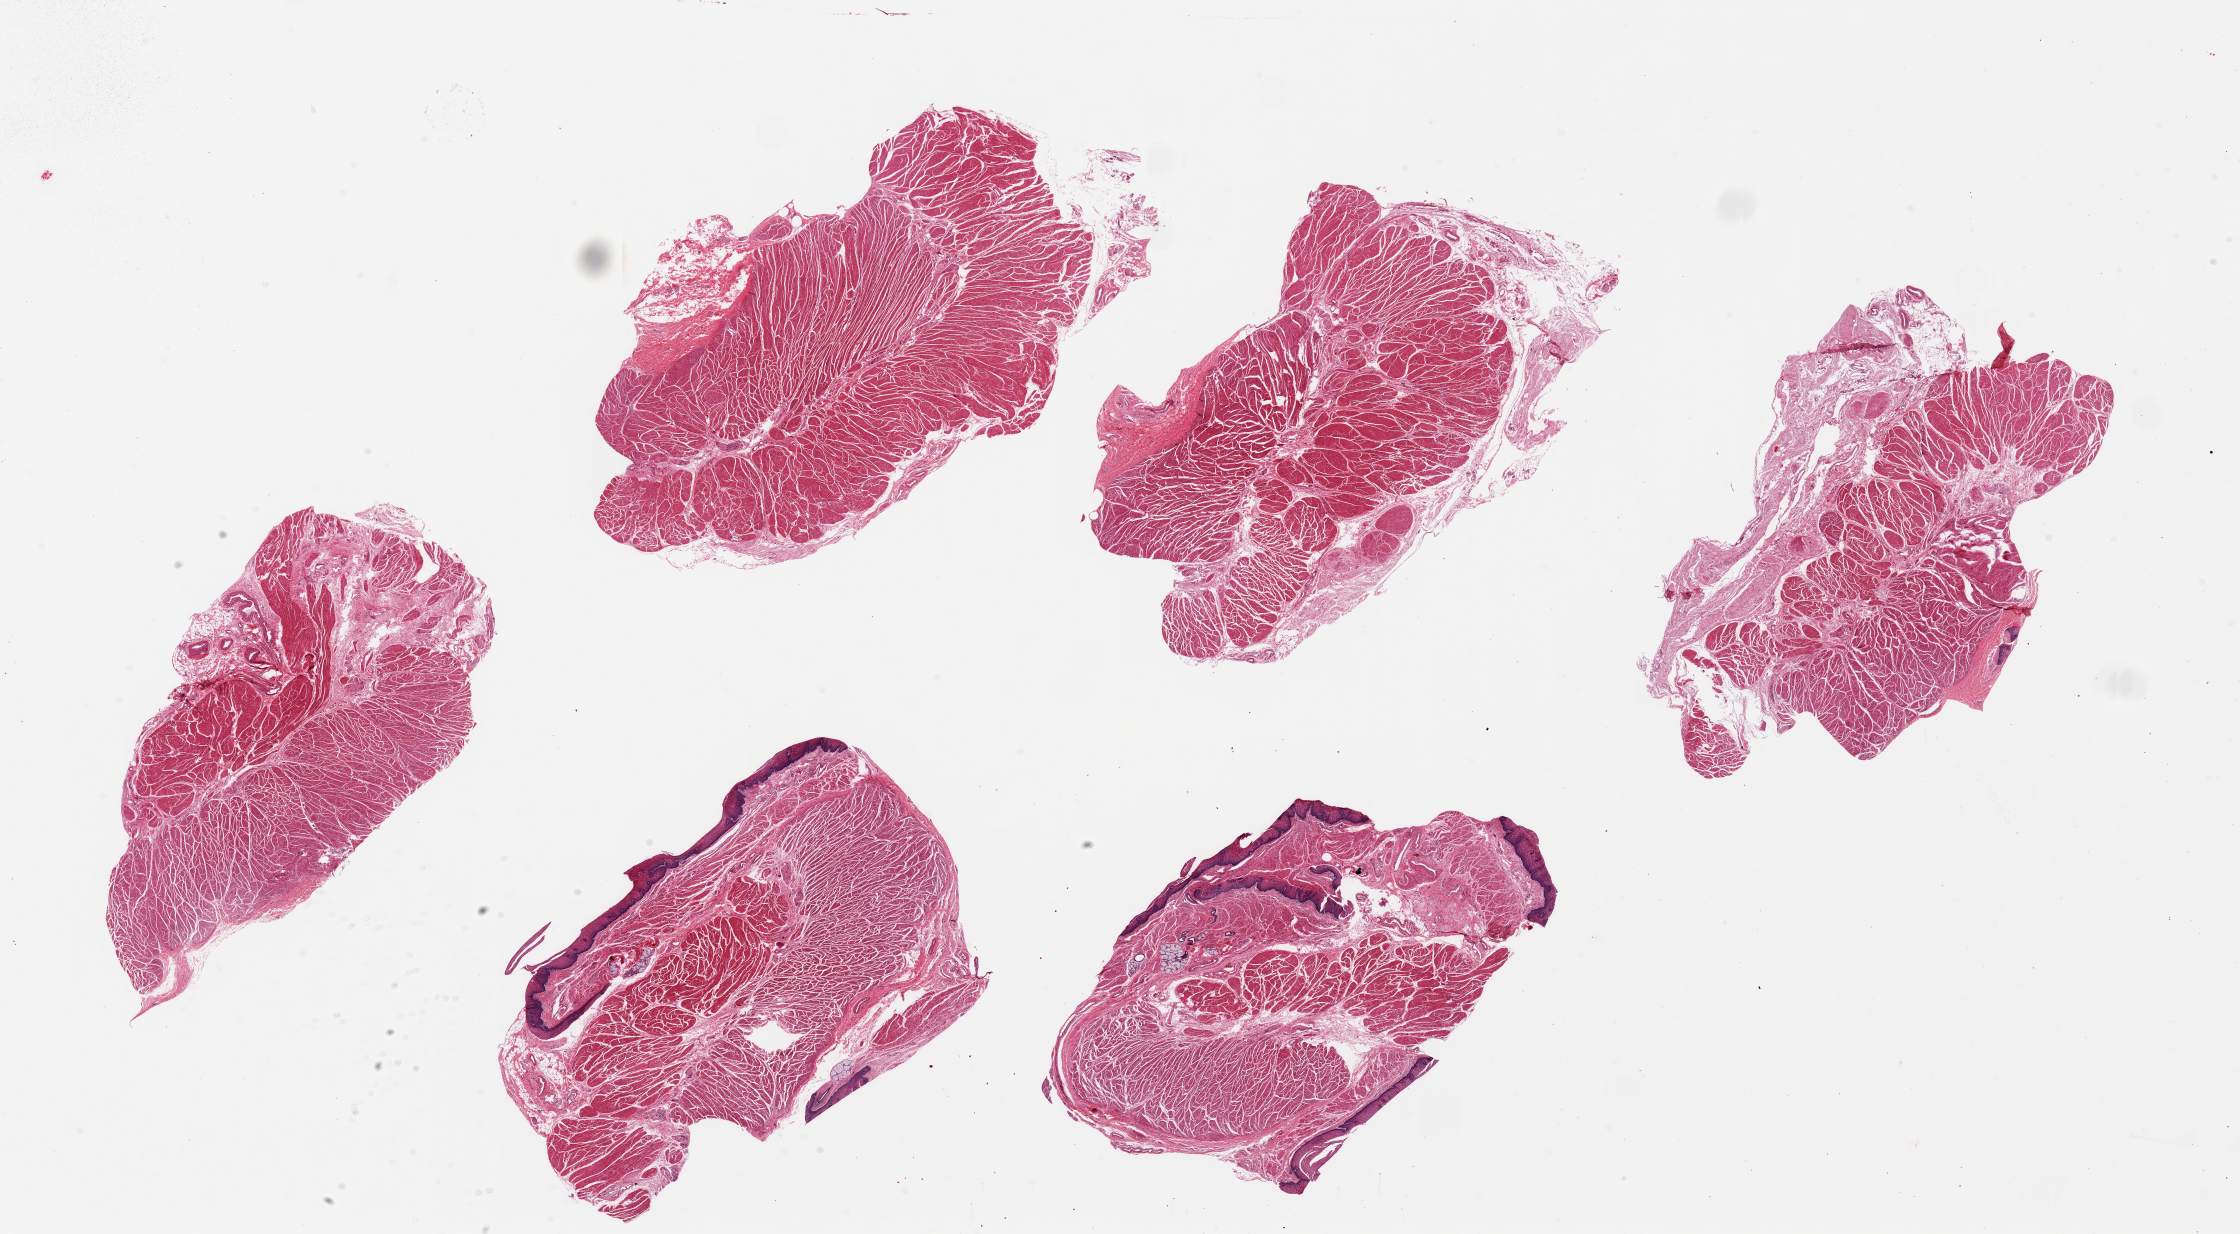
H&E whole-slide image, brightfield, a low-resolution overview of the entire scanned area, about 35.4 x 19.5 mm (acquisition: 20x scan). PAXgene-fixed, paraffin-embedded tissue. Section of gastroesophageal junction (target tissue). Tissue donor sample.
Pathologist's review note for this sample: 6 pieces, up to 10x6mm; 2 have squamous mucosa.